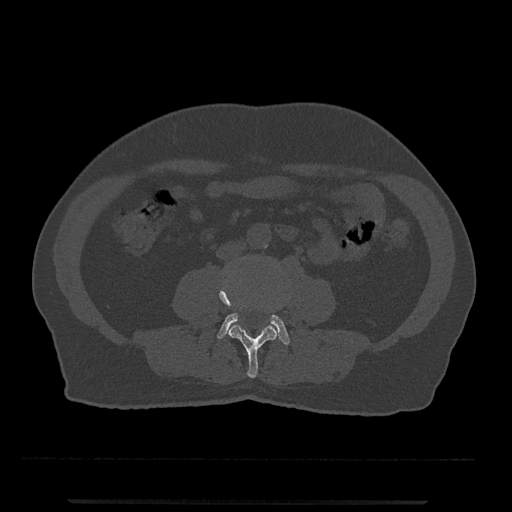
CT including the spine, one axial slice. Reconstruction kernel Br40s/3. 120 kVp. Bone window (W 1800 / L 400 HU). 0.5 mm slice thickness. 512 × 512 image matrix, field of view 419 × 419 mm. Patient: male, 63 years. From the clinical record (not read from this slice): primary cancer: prostate.
Structures marked on this image (semi-automatically segmented with operator editing):
- L3 vertebra: box from (x=219, y=280) to (x=277, y=378) px
- L4 vertebra: (x=217, y=313)–(x=290, y=345)